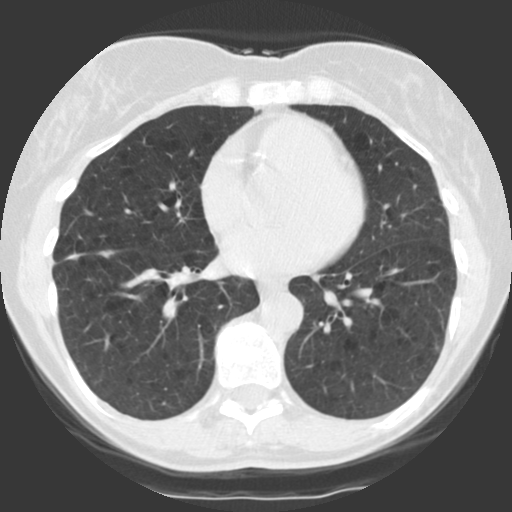
Low-dose screening chest CT, one axial slice; position 53 of 123 along the scan axis; reconstruction kernel STANDARD; 140 kVp; lung window (W 1500 / L -600 HU); 512 × 512 image matrix, field of view 290 × 290 mm.
Structures marked on this image (expert manual segmentation):
- lesion 1 (tumor, middle lobe of right lung): box from (x=66, y=253) to (x=83, y=260) px